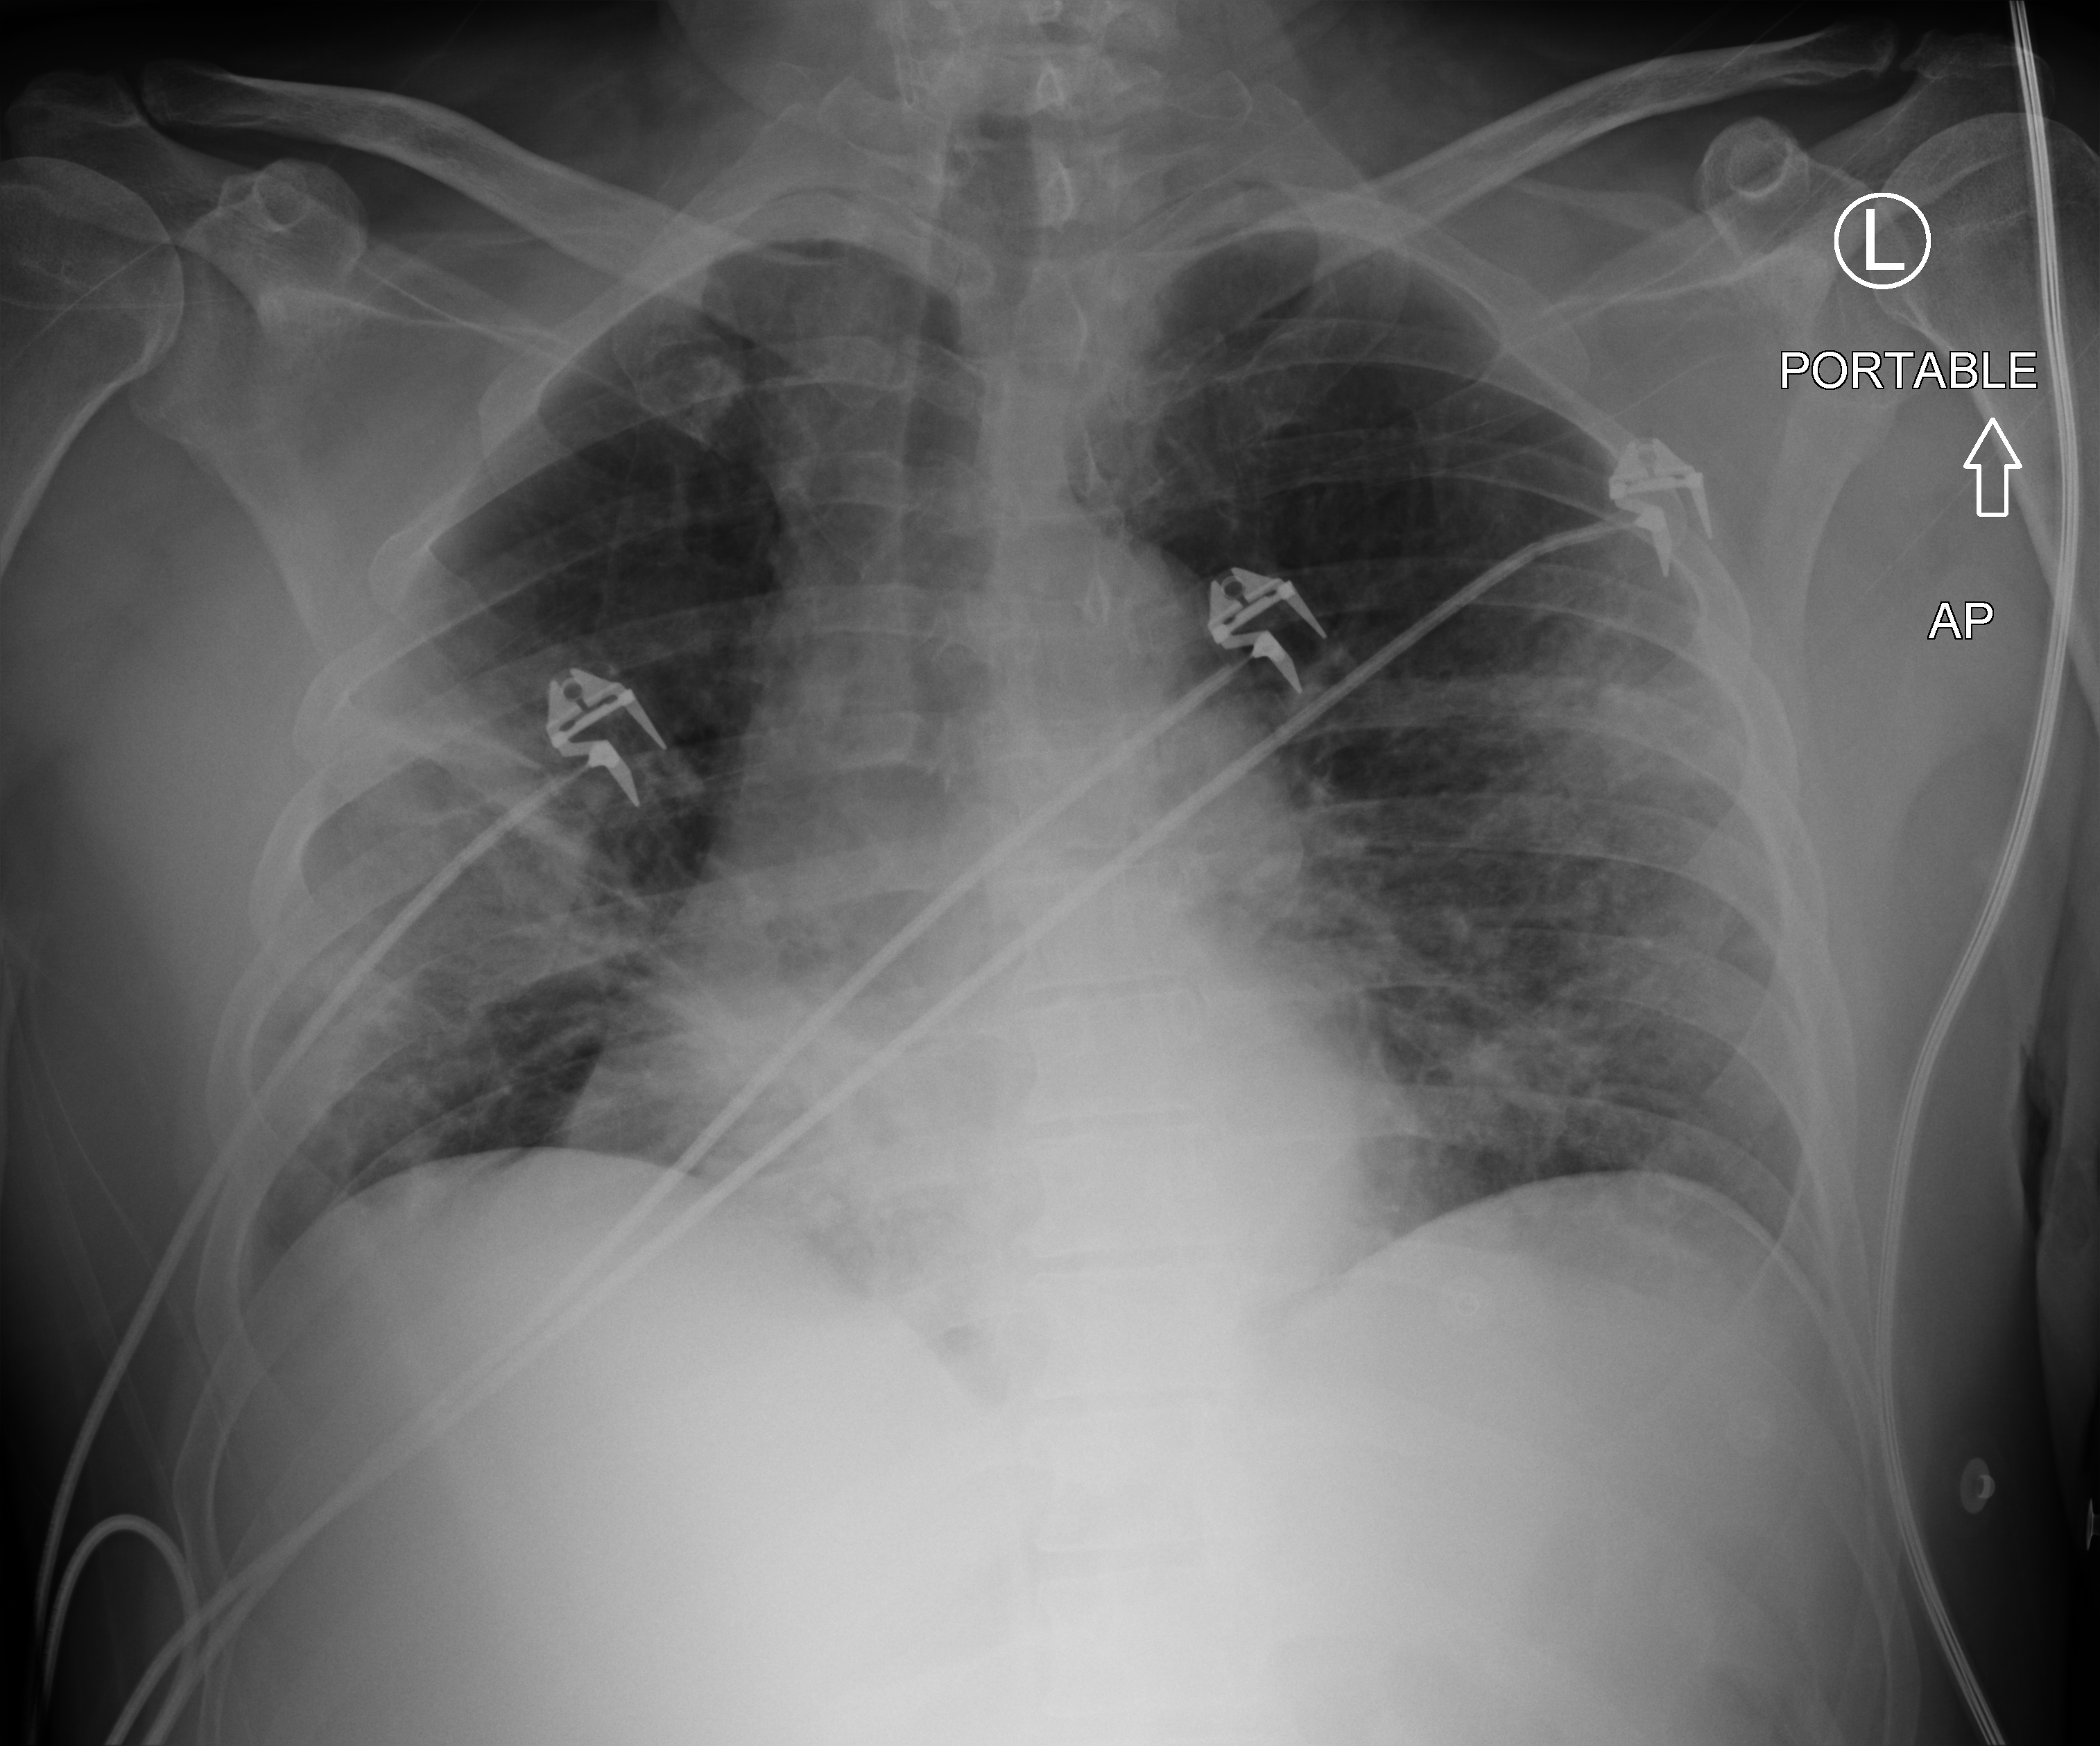
Portable chest radiograph. Male patient hospitalised with COVID-19, age 60–74 years.
Hospital-stay facts (about this admission, not read from this image; timing relative to this image not recorded):
- smoking status (admission record): never